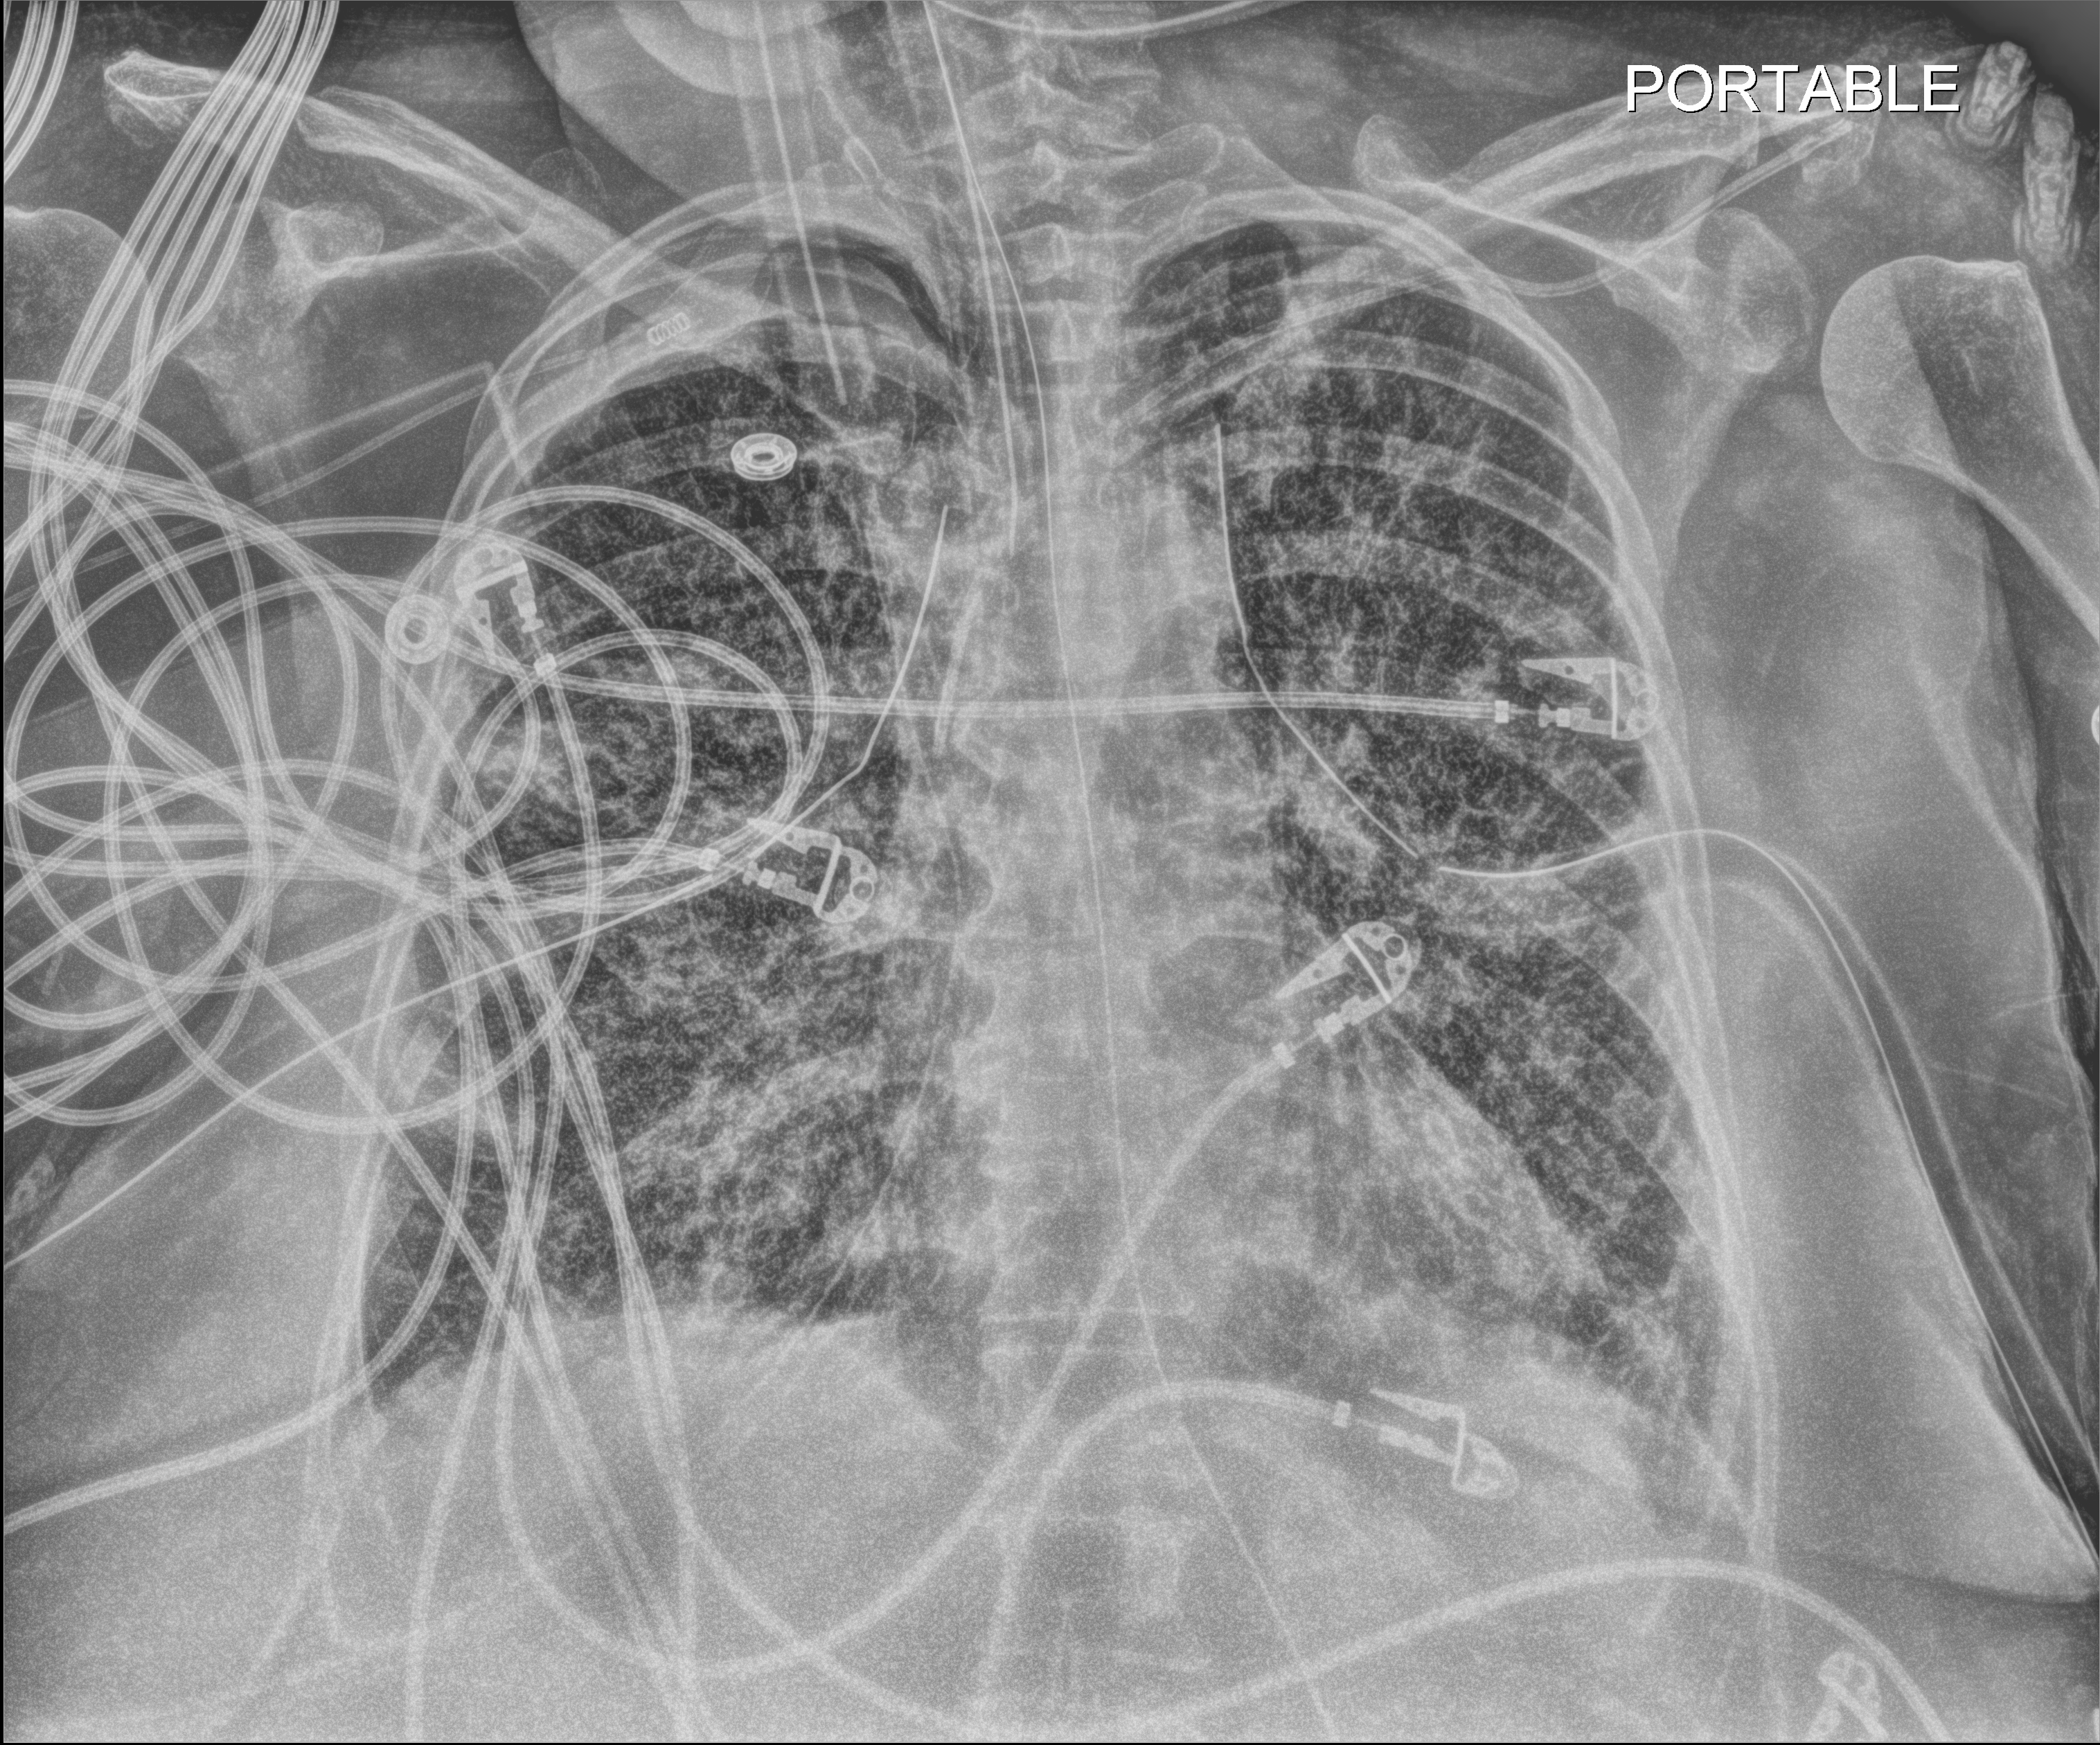
Portable chest radiograph; anteroposterior (AP) projection. Female patient hospitalised with COVID-19, age 60–74 years.
Hospital-stay facts (about this admission, not read from this image; timing relative to this image not recorded): admitted to intensive care during this hospital stay: yes; length of hospital stay: 38 days.